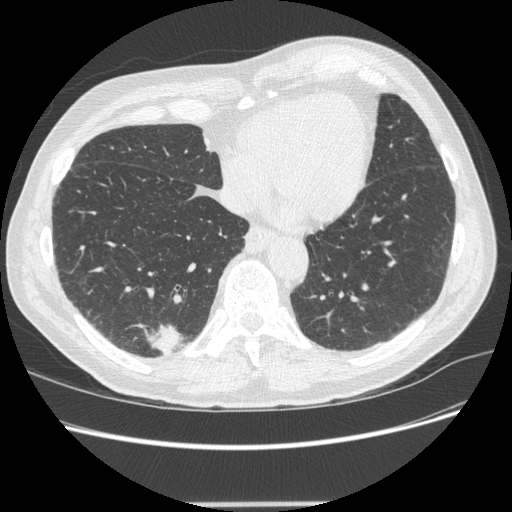
Low-dose screening chest CT, one axial slice; position 72 of 245 along the scan axis; reconstruction kernel STANDARD; 120 kVp; lung window (W 1500 / L -600 HU); 1.25 mm slice thickness; 512 × 512 image matrix, field of view 372 × 372 mm.
Outlined on this slice (expert manual segmentation):
- lesion 1 (tumor, lower lobe of right lung): bounding box [x1, y1, x2, y2] px = [149, 324, 183, 356]